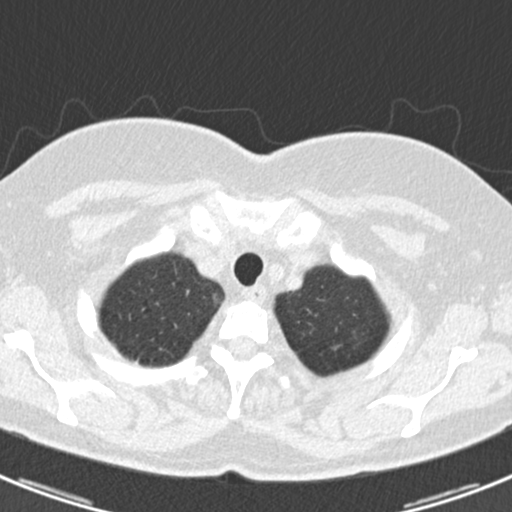
Chest CT (low-dose screening protocol), one axial image; baseline screening round; lung window (W 1500 / L -600 HU); 2 mm slice thickness; standard (soft-tissue) reconstruction kernel (B30f); 120 kVp; 512 × 512 image matrix. Female participant, aged 60 years at enrolment.
Expert reader's lesion annotation, bounding box <333,321,375,360> (left, top, right, bottom; pixels). The screening reader recorded 3 non-calcified nodules or masses ≥4 mm on this exam (lingula, left lower lobe, lingula); which of them this box marks is not recorded. Official screen result: positive, change unspecified: nodule(s) >= 4 mm or enlarging nodule(s), mass(es), or other non-specific abnormalities suspicious for lung cancer.